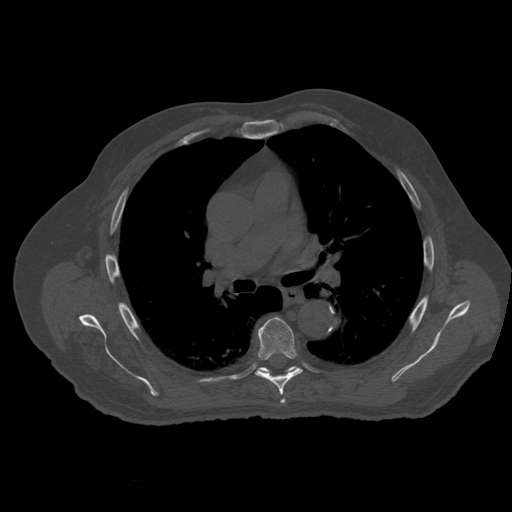
CT including the spine, one axial slice. Position 378 of 399 along the scan axis. Reconstruction kernel STANDARD. 120 kVp. Bone window (W 1800 / L 400 HU). 512 × 512 image matrix, field of view 407 × 407 mm. Patient age 73 years. From the clinical record (not read from this slice): primary cancer: prostate; vertebrae with lytic lesions (as recorded): L2.
Annotated regions visible in this slice (semi-automatically segmented with operator editing):
- T5 vertebra: box from (x=281, y=399) to (x=286, y=404) px
- T6 vertebra: (x=256, y=317)–(x=303, y=396)
- T7 vertebra: (x=259, y=366)–(x=297, y=374)